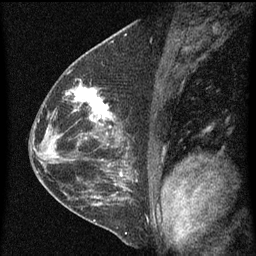
Breast MRI (dynamic contrast-enhanced), one sagittal slice; position 31 of 60 along the scan axis; dynamic contrast-enhanced series, image 2 of 4 at this slice position (ordered by acquisition); 1.5 T; TE 4.2 ms, TR 8 ms; 2 mm slice thickness; 256 × 256 image matrix, field of view 180 × 180 mm. Female patient, age 48 years.
Structures marked on this image (semi-automatic segmentation, software-assisted and operator-edited):
- analysis volume of interest (the breast-tissue region the enhancement analysis was run in; not a lesion): bounding box [x1, y1, x2, y2] px = [73, 82, 115, 139]
- tumour enhancement mask (voxels above the 70 % enhancement threshold inside the analysis volume of interest): [74, 82, 112, 129]